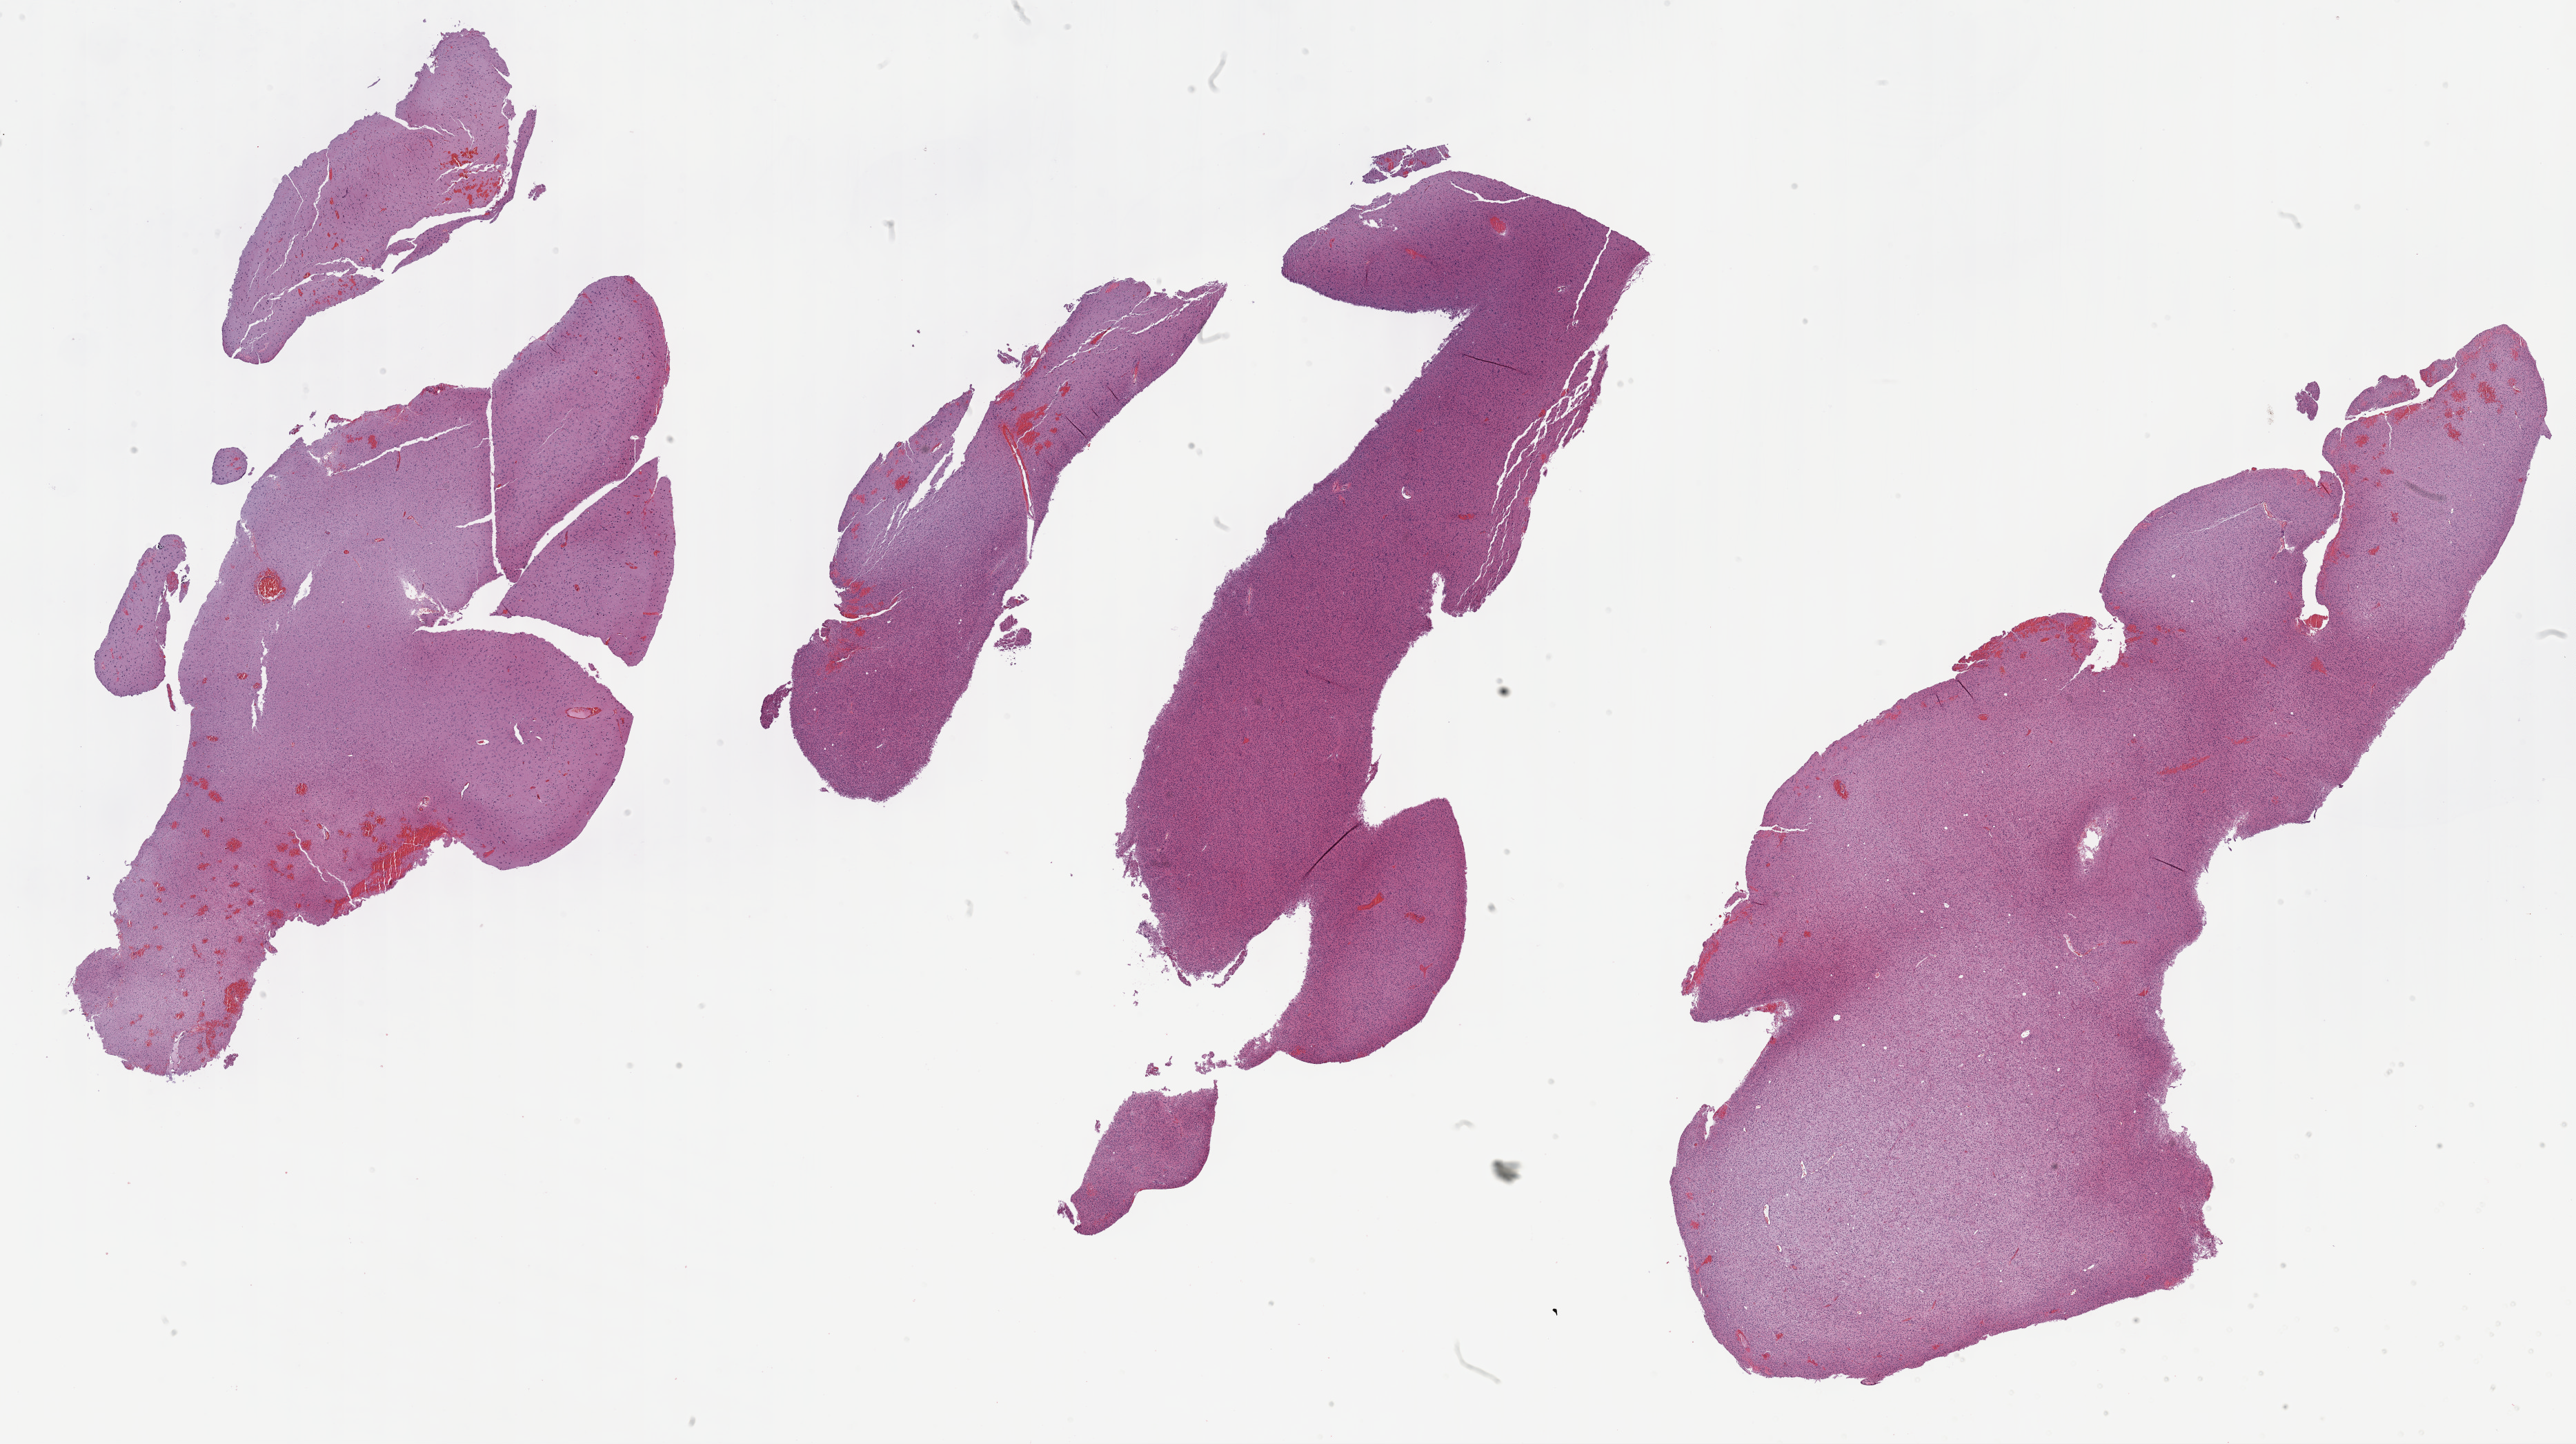
Whole-slide histology image, H&E-stained — whole scanned area (about 30.2 x 16.9 mm, acquisition: 40x scan) shown as a low-resolution overview, formalin-fixed paraffin-embedded (FFPE) diagnostic section, sample: primary tumour, brain. Male, age 25 years at initial diagnosis. Histologic grade: G2 (moderately differentiated).
* pathologic diagnosis: Oligodendroglioma, NOS (cerebrum)
* laterality: left